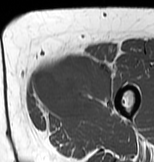
MRI of an extremity soft-tissue mass, one axial slice. Position 21 of 83 along the scan axis. MR volume resampled by the dataset authors to the PET/CT grid (not the native acquisition matrix). 3.27 mm slice thickness. 154 × 162 image matrix, field of view 150 × 158 mm. Female patient. Case-level facts recorded for this patient, not image findings: histological type: myxofibrosarcoma; grade: intermediate; site of the primary tumour: left thigh.
Annotated regions visible in this slice (expert contour drawn on MRI and transferred to this co-registered scan by the dataset authors):
- gross tumour volume including surrounding oedema: bounding box [x1, y1, x2, y2] px = [30, 52, 114, 122]
- gross tumour volume (mass): [33, 55, 113, 122]